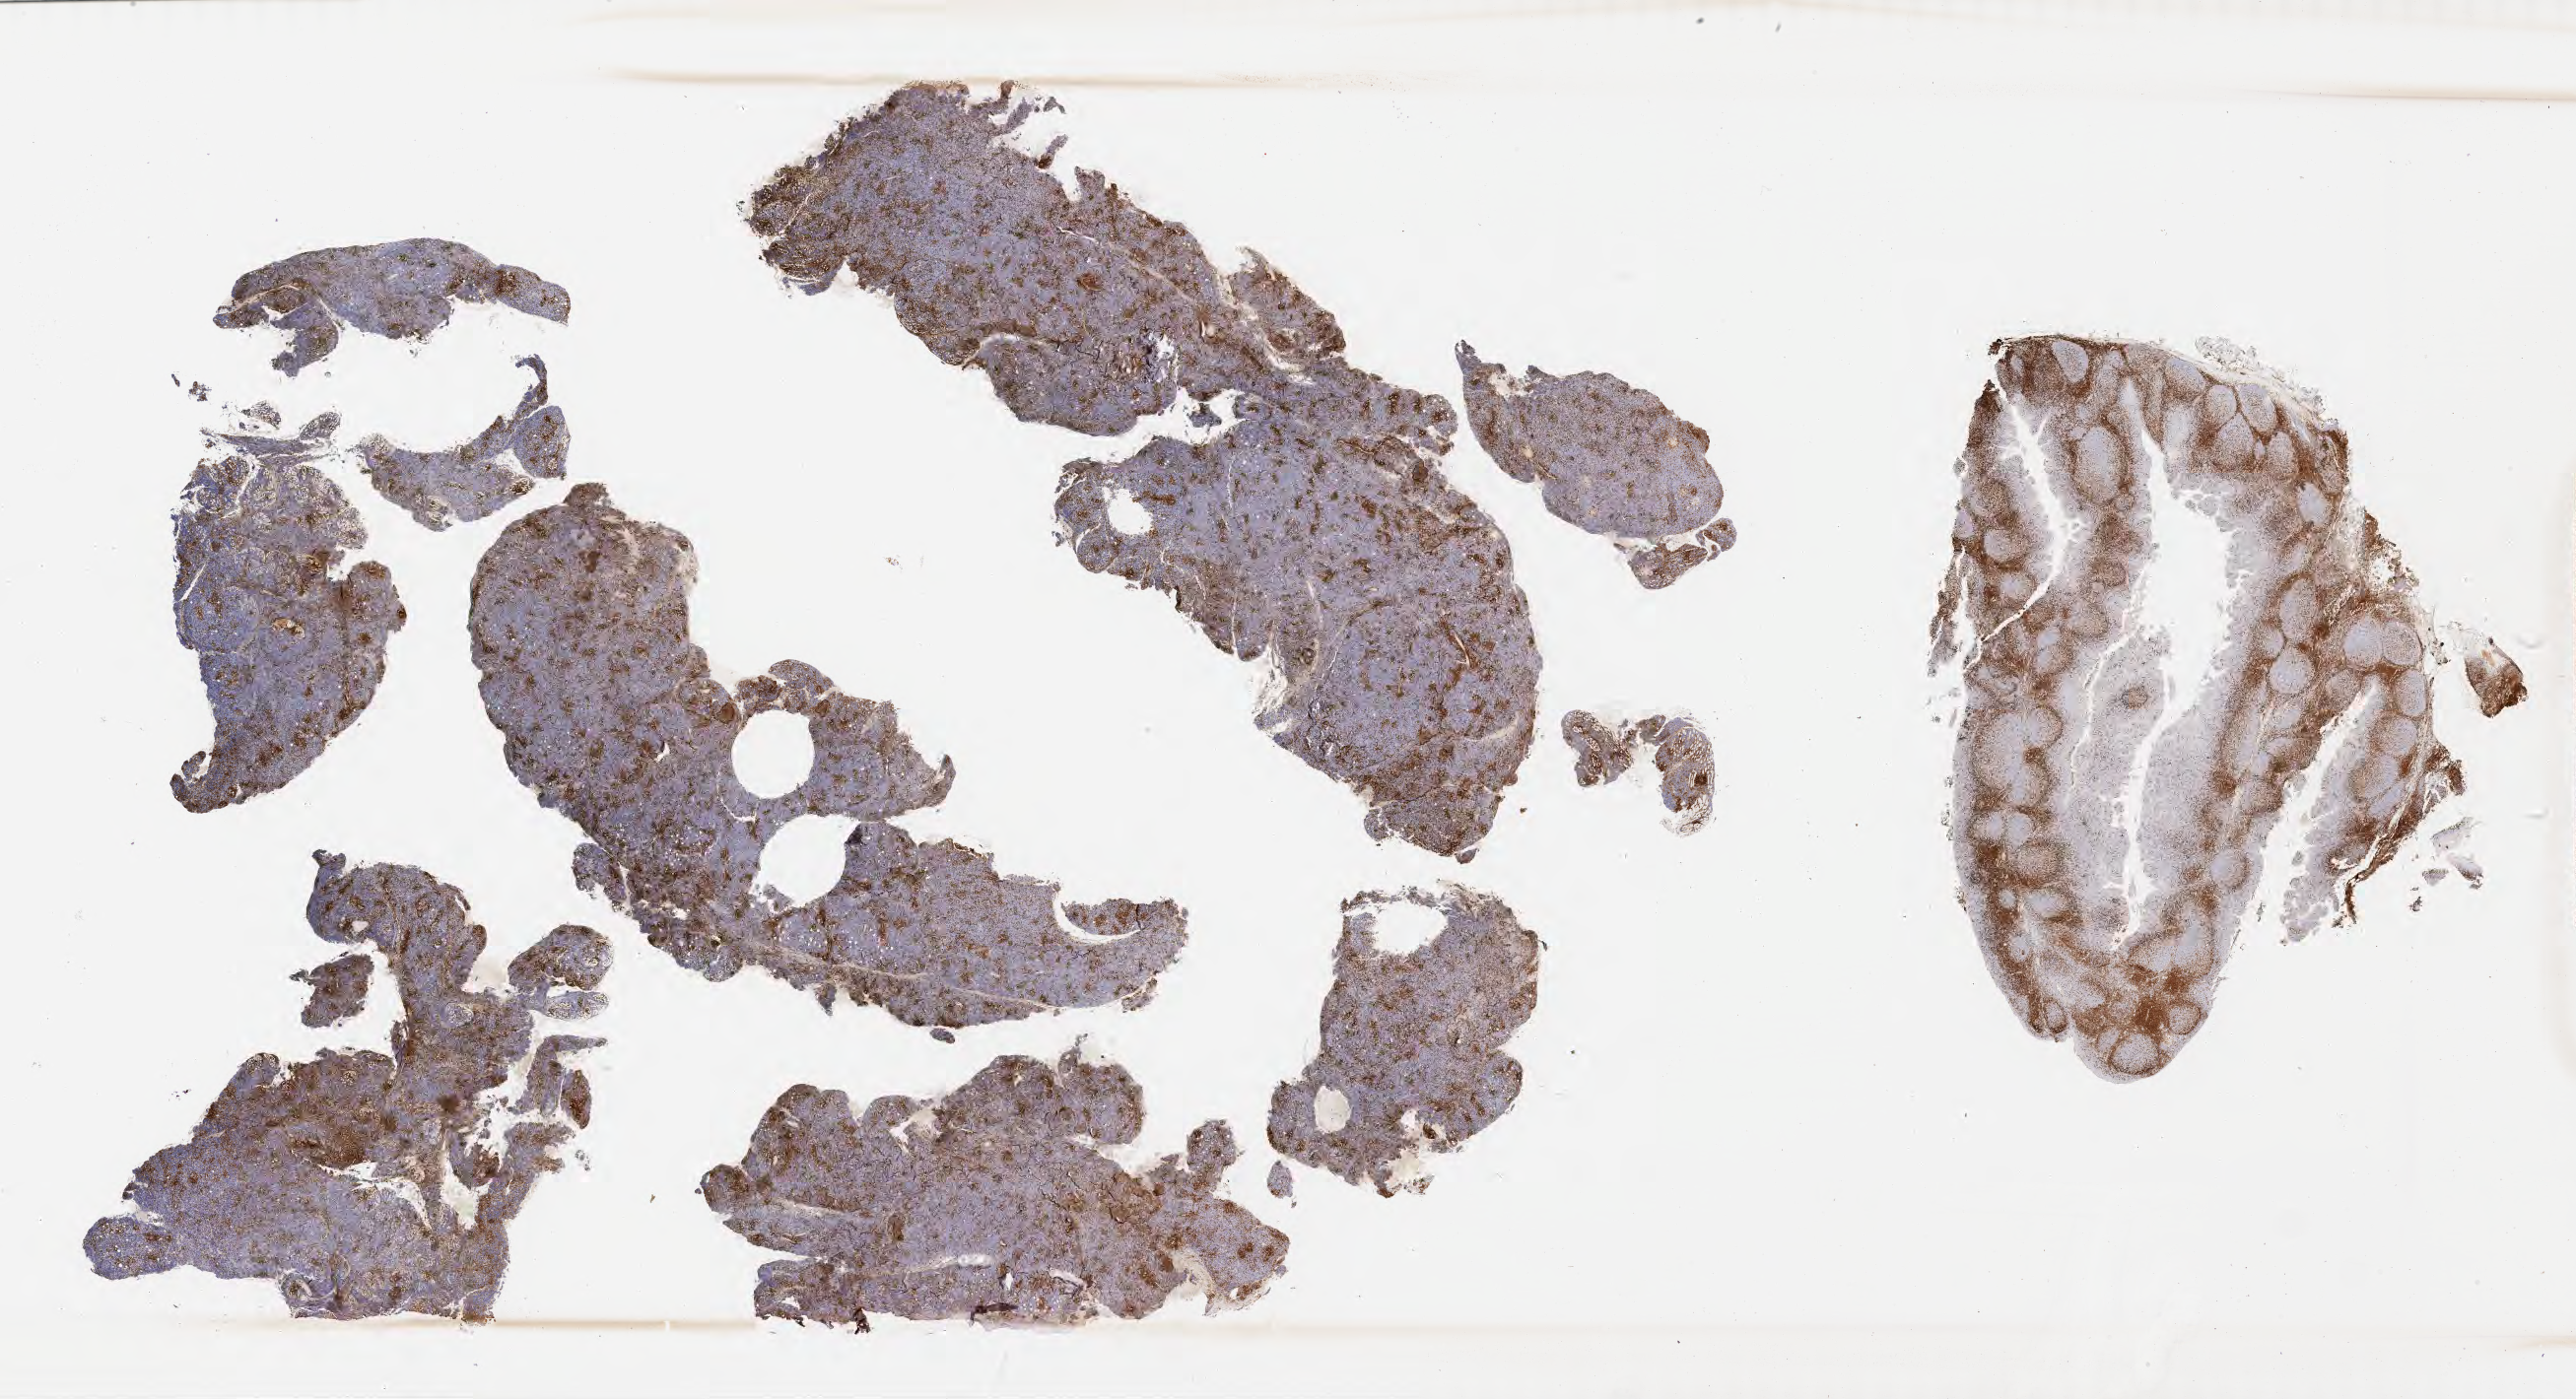
IHC for CD3, whole-slide image, whole scanned area (about 42.3 x 23.0 mm) shown as a low-resolution overview. Tumor tissue. Site: cranium. Male patient; age at initial diagnosis 5 years.
- diagnosis: Burkitt lymphoma, NOS